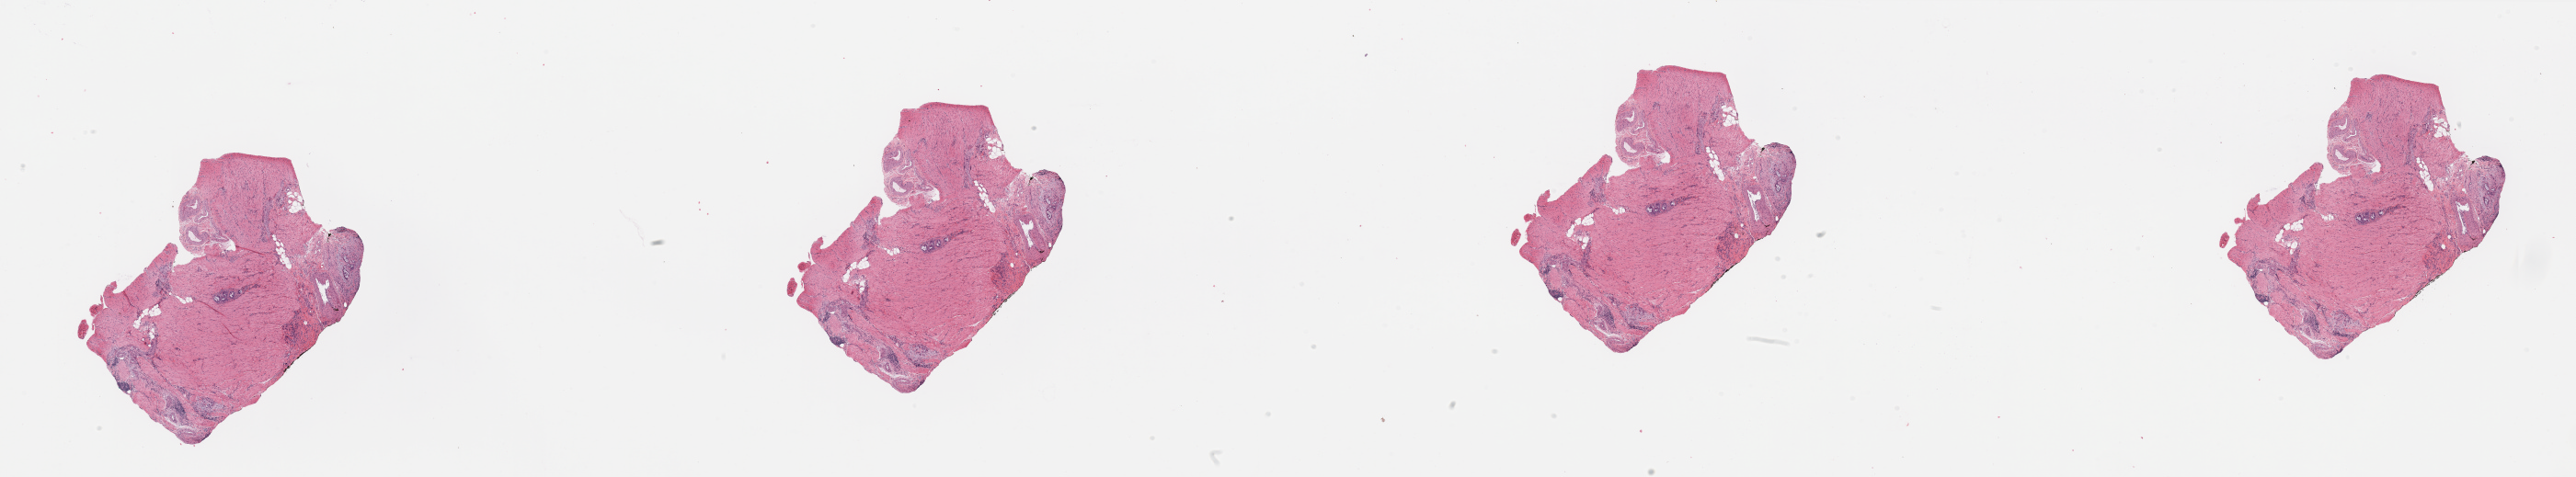
H&E-stained whole-slide image — whole scanned area (about 44.3 x 8.2 mm, slide scanned at 20x) shown as a low-resolution overview; tumour tissue sample, pancreas. Female, 74 y/o.
Patient diagnosis (cohort enrolment): ductal adenocarcinoma (pancreas).